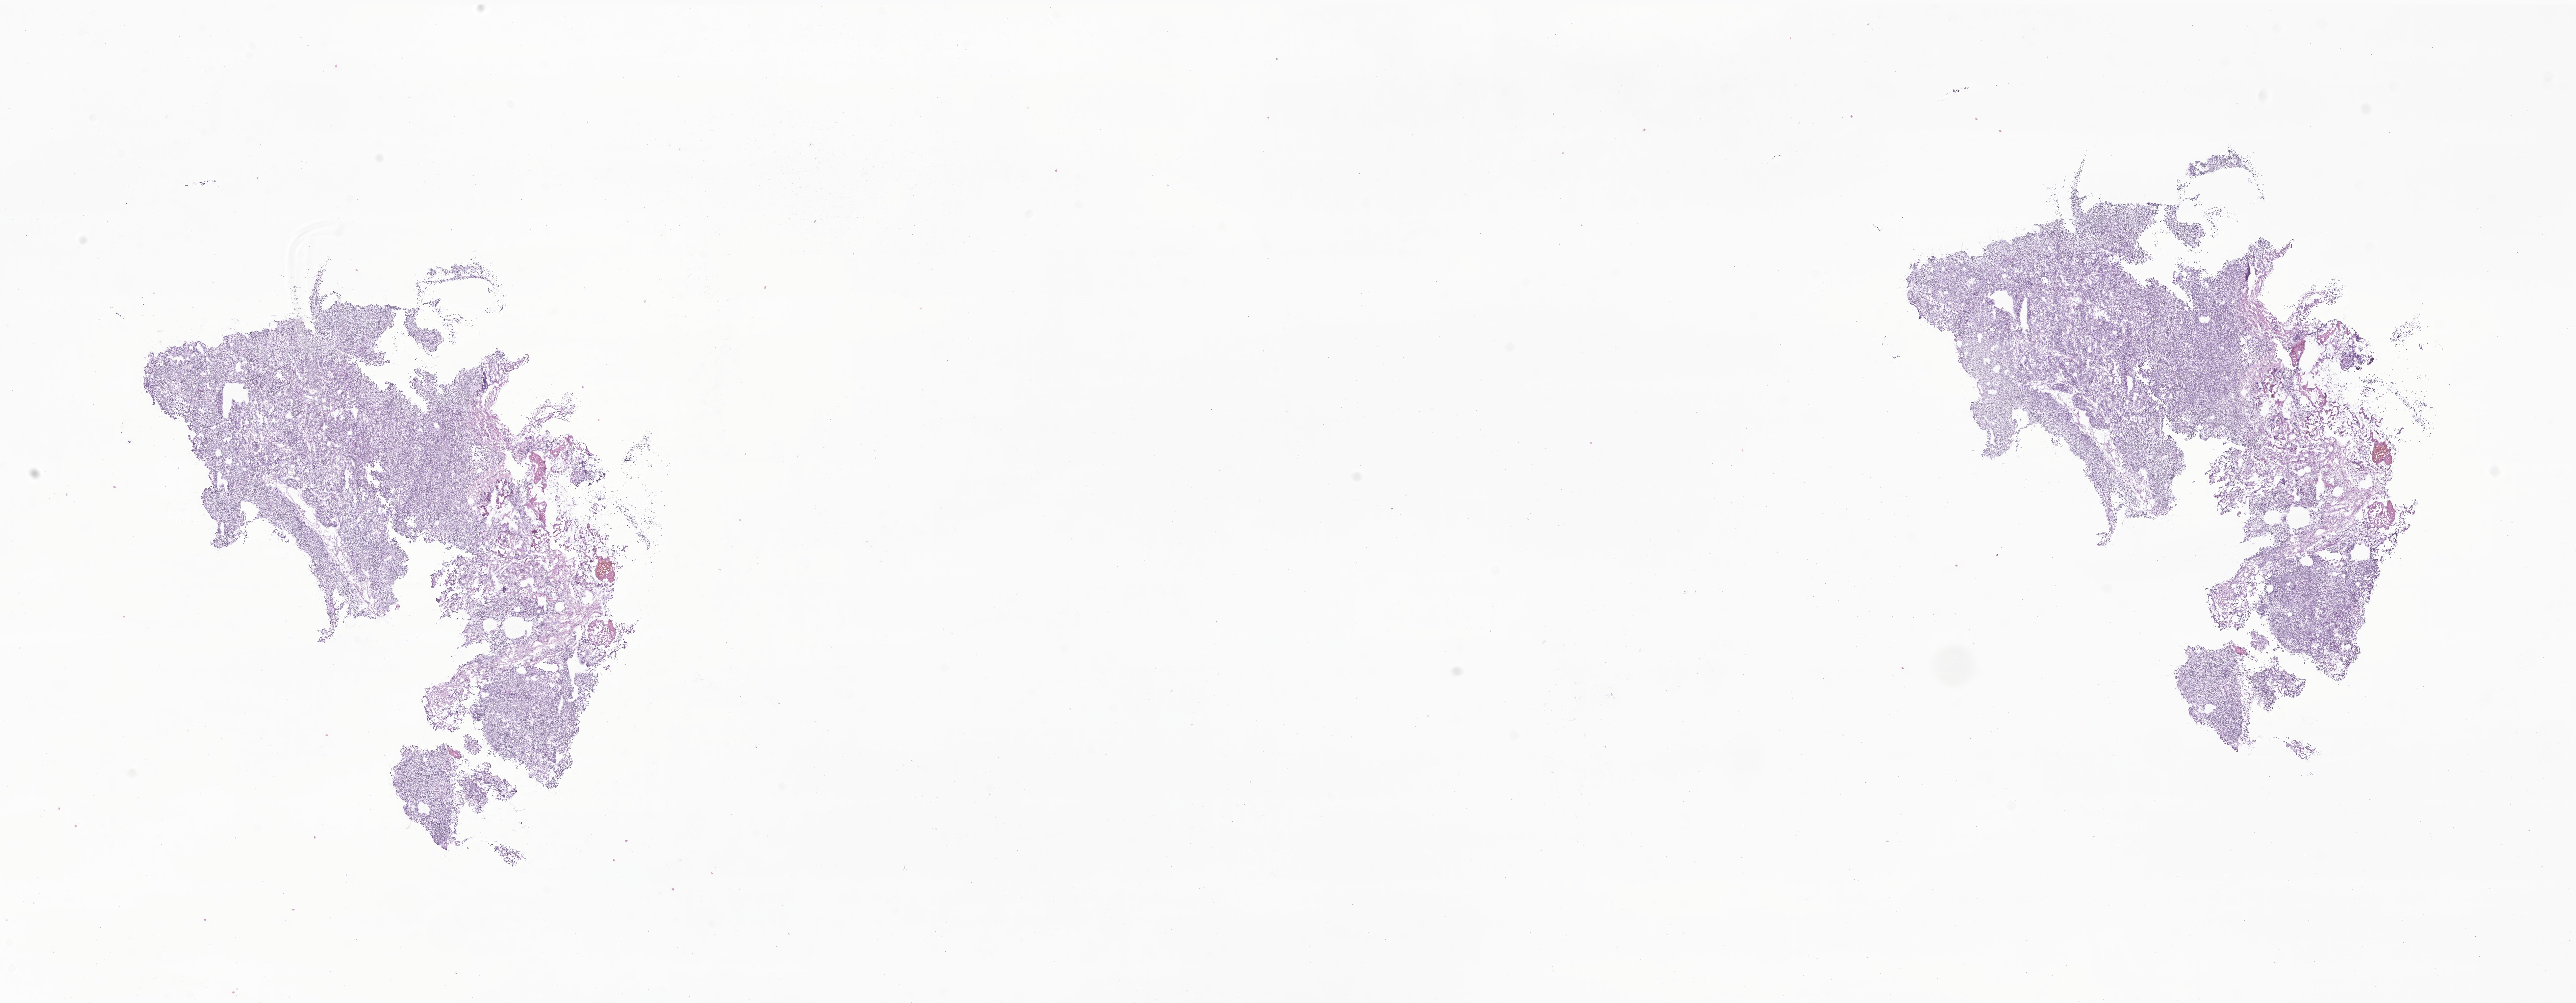
Haematoxylin and eosin whole-slide image of tumor tissue from the cerebellum, whole scanned area (about 33.0 x 12.8 mm) shown as a low-resolution overview, cryosection (OCT / tissue freezing medium). Male patient, age 60 months (5 years).
* diagnosis: Medulloblastoma, NOS